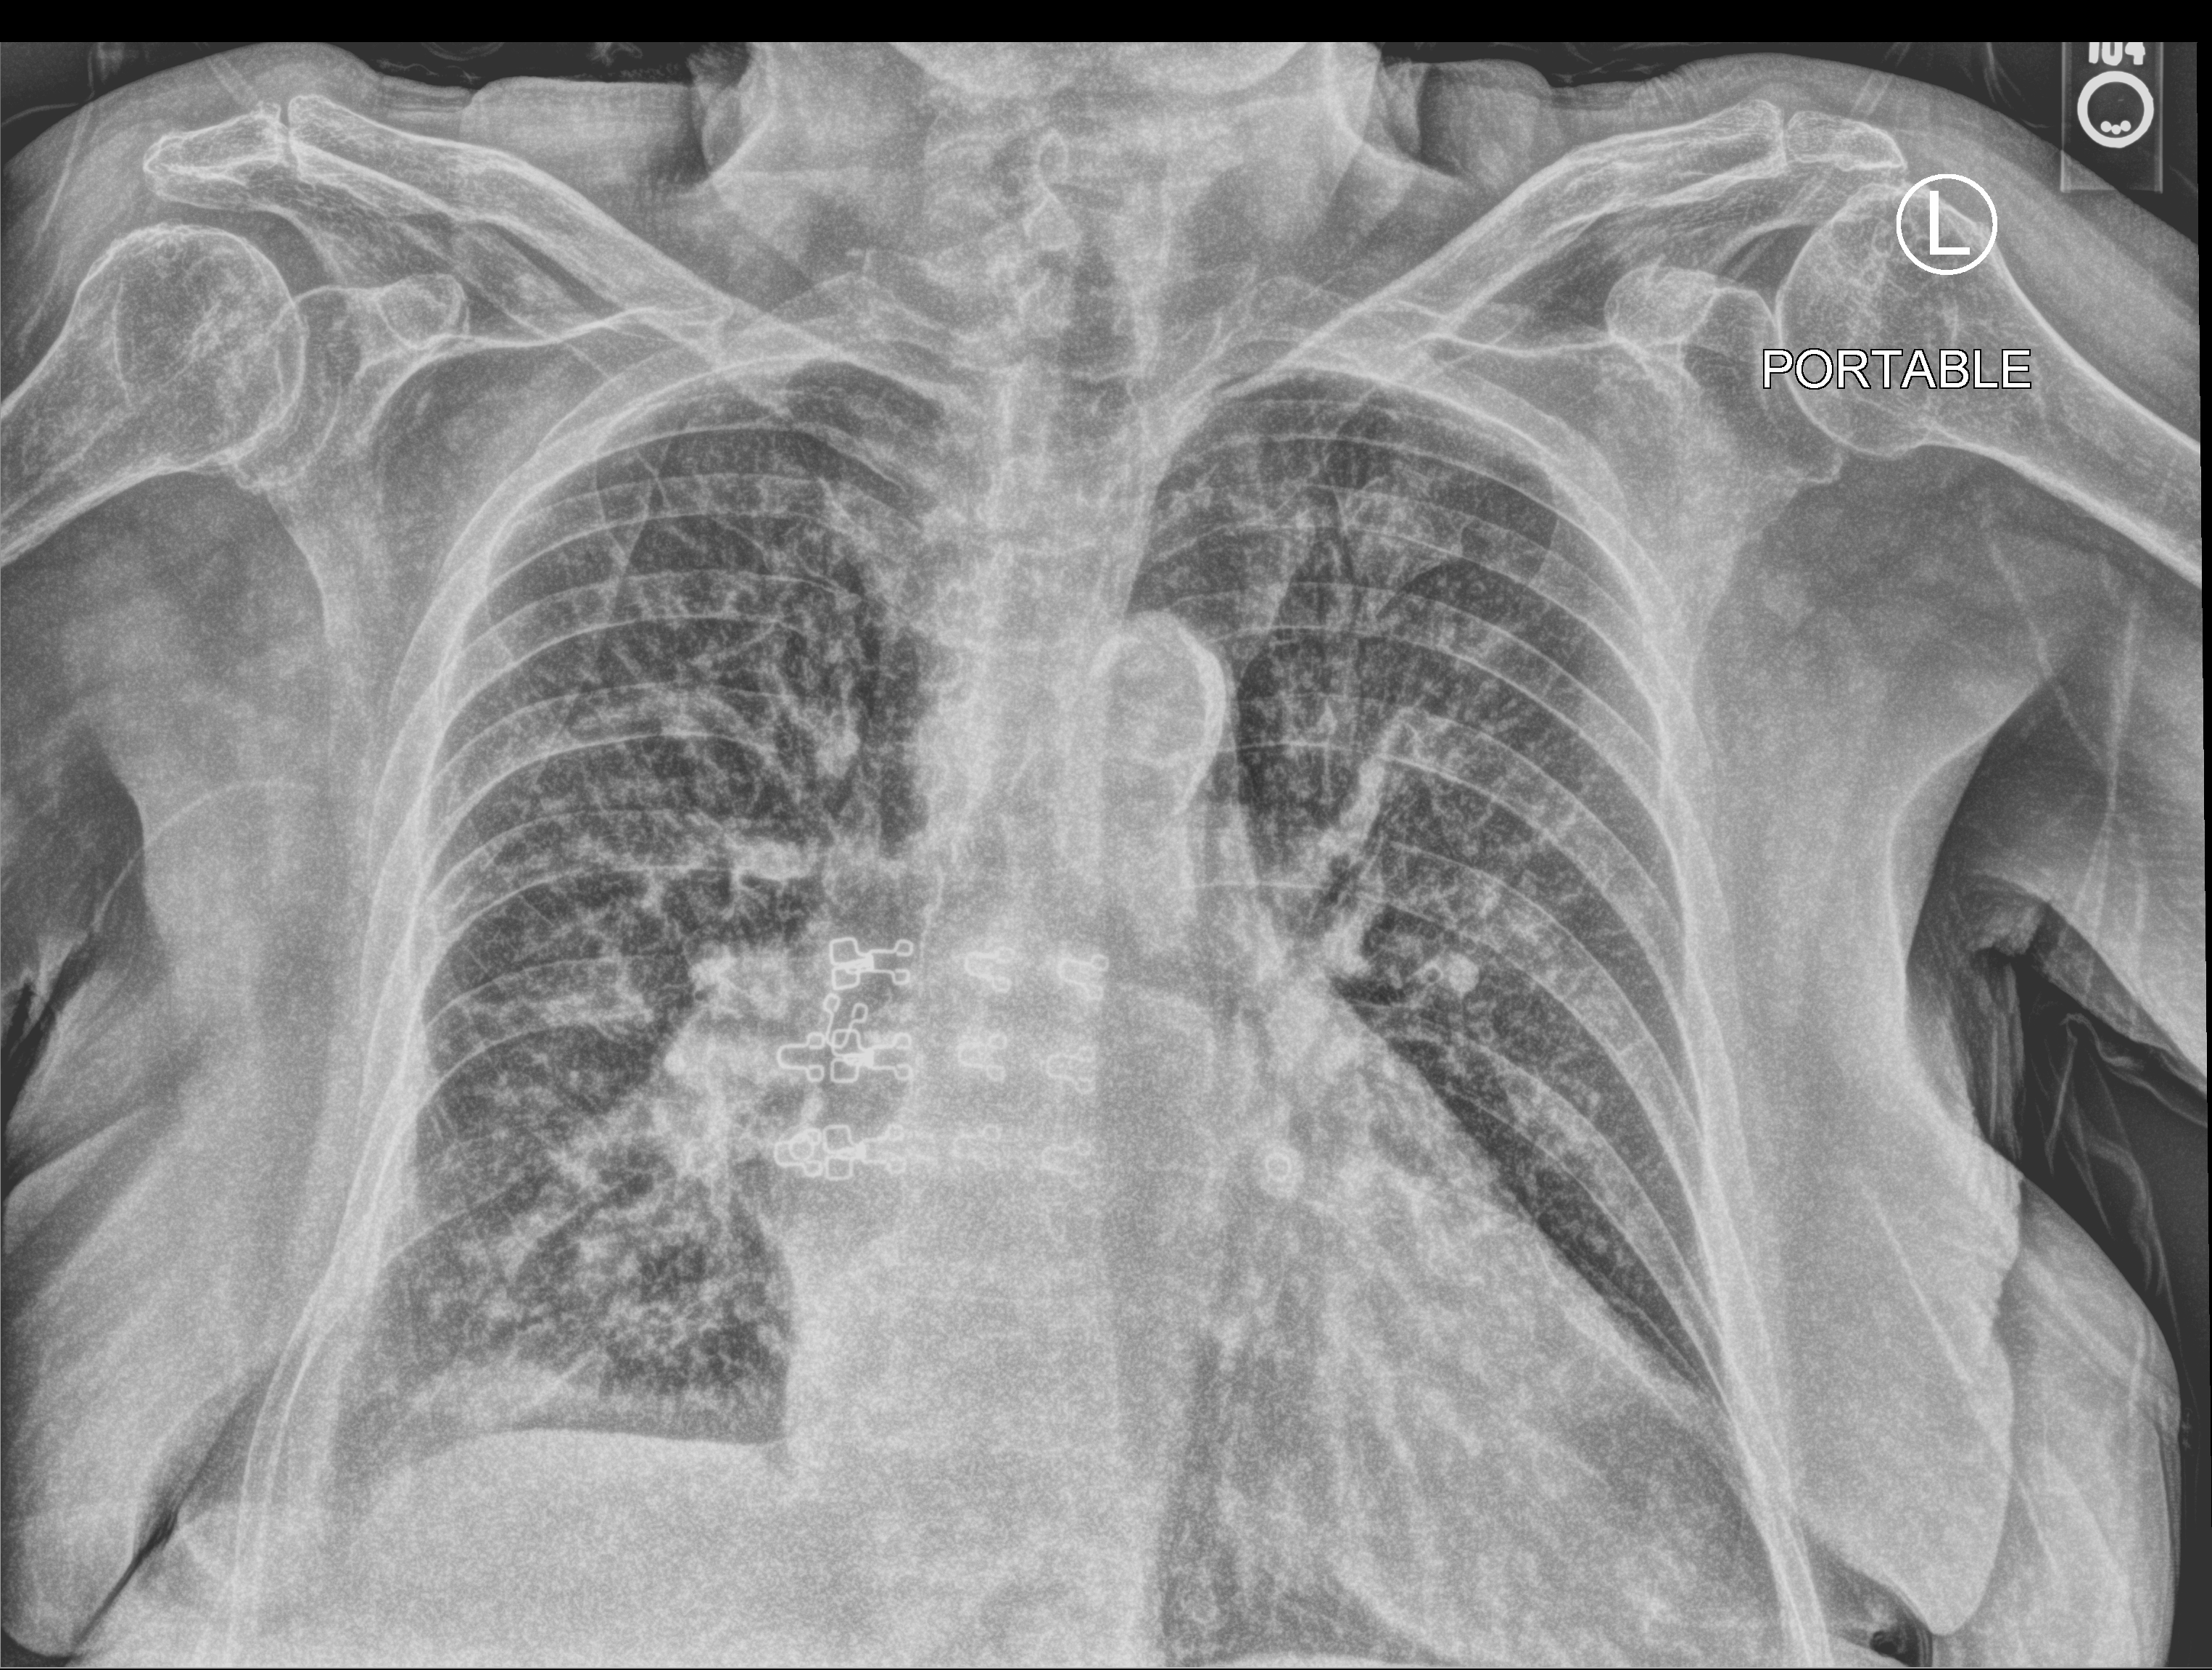
Portable chest radiograph, anteroposterior (AP) projection. Patient hospitalised with COVID-19; female, aged 75–90 years.
Hospital-stay facts (about this admission, not read from this image; timing relative to this image not recorded): mechanically ventilated during this hospital stay: no.